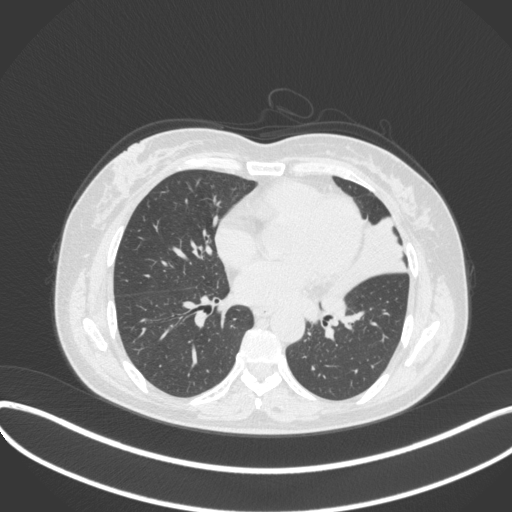
Chest CT, one axial slice; position 161 of 373 along the scan axis; reconstruction kernel B31f; 120 kVp; lung window (W 1500 / L -600 HU); 1 mm slice thickness; 512 × 512 image matrix, field of view 400 × 400 mm. Patient: female, 54 years. From the clinical record (not read from this slice): clinical TNM (as recorded): T2a N1 M0; histopathological grade: G3.
Structures marked on this image (rectangle marked by the reading radiologist):
- lung tumour (recorded histology: small cell carcinoma): box from (x=318, y=271) to (x=360, y=325) px